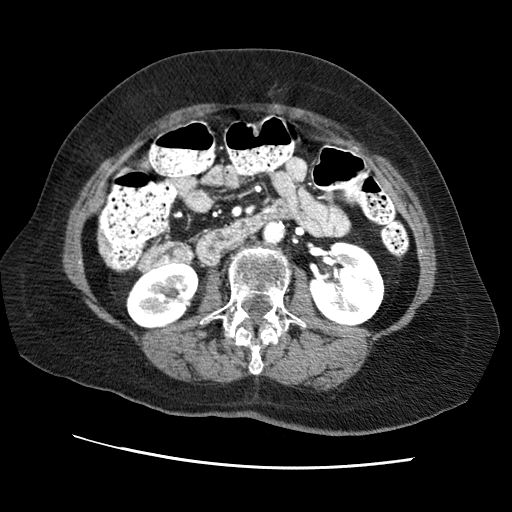
Contrast-enhanced abdominal CT (liver protocol), one axial slice. Slice 10 of 65 in the series (ordered by position). Reconstruction kernel STANDARD. 120 kVp. Soft-tissue window (W 400 / L 40 HU). 512 × 512 image matrix, field of view 340 × 340 mm. From the clinical record (not read from this slice): diagnosis: hepatocellular carcinoma (patient treated with transarterial chemoembolisation; whether this scan precedes or follows treatment is not stated here); TNM stage (as recorded): Stage-II.
Annotated regions visible in this slice (semi-automatically segmented with operator editing):
- liver parenchyma outside the tumour (the mass and vessels are separate outlines, so this box may not span the whole liver): bounding box <98,237,108,255> (left, top, right, bottom; pixels)